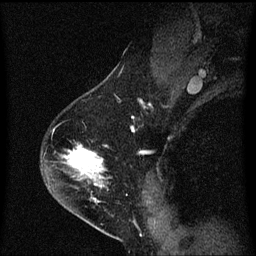
Breast MRI (dynamic contrast-enhanced), one sagittal slice. Position 43 of 60 along the scan axis. Dynamic contrast-enhanced series, image 2 of 3 at this slice position (ordered by acquisition). 1.5 T. TE 4.2 ms, TR 8.4 ms. 256 × 256 image matrix. Female patient, age 54 years. From the clinical record (not read from this slice): setting: breast cancer imaged before/during neoadjuvant chemotherapy; receptor status: HER2-positive.
Outlined on this slice (semi-automatically segmented with operator editing):
- analysis volume of interest (the breast-tissue region the enhancement analysis was run in; not a lesion): bounding box <42,146,111,213> (left, top, right, bottom; pixels)
- tumour enhancement mask (voxels above the 70 % enhancement threshold inside the analysis volume of interest): <70,148,103,173>